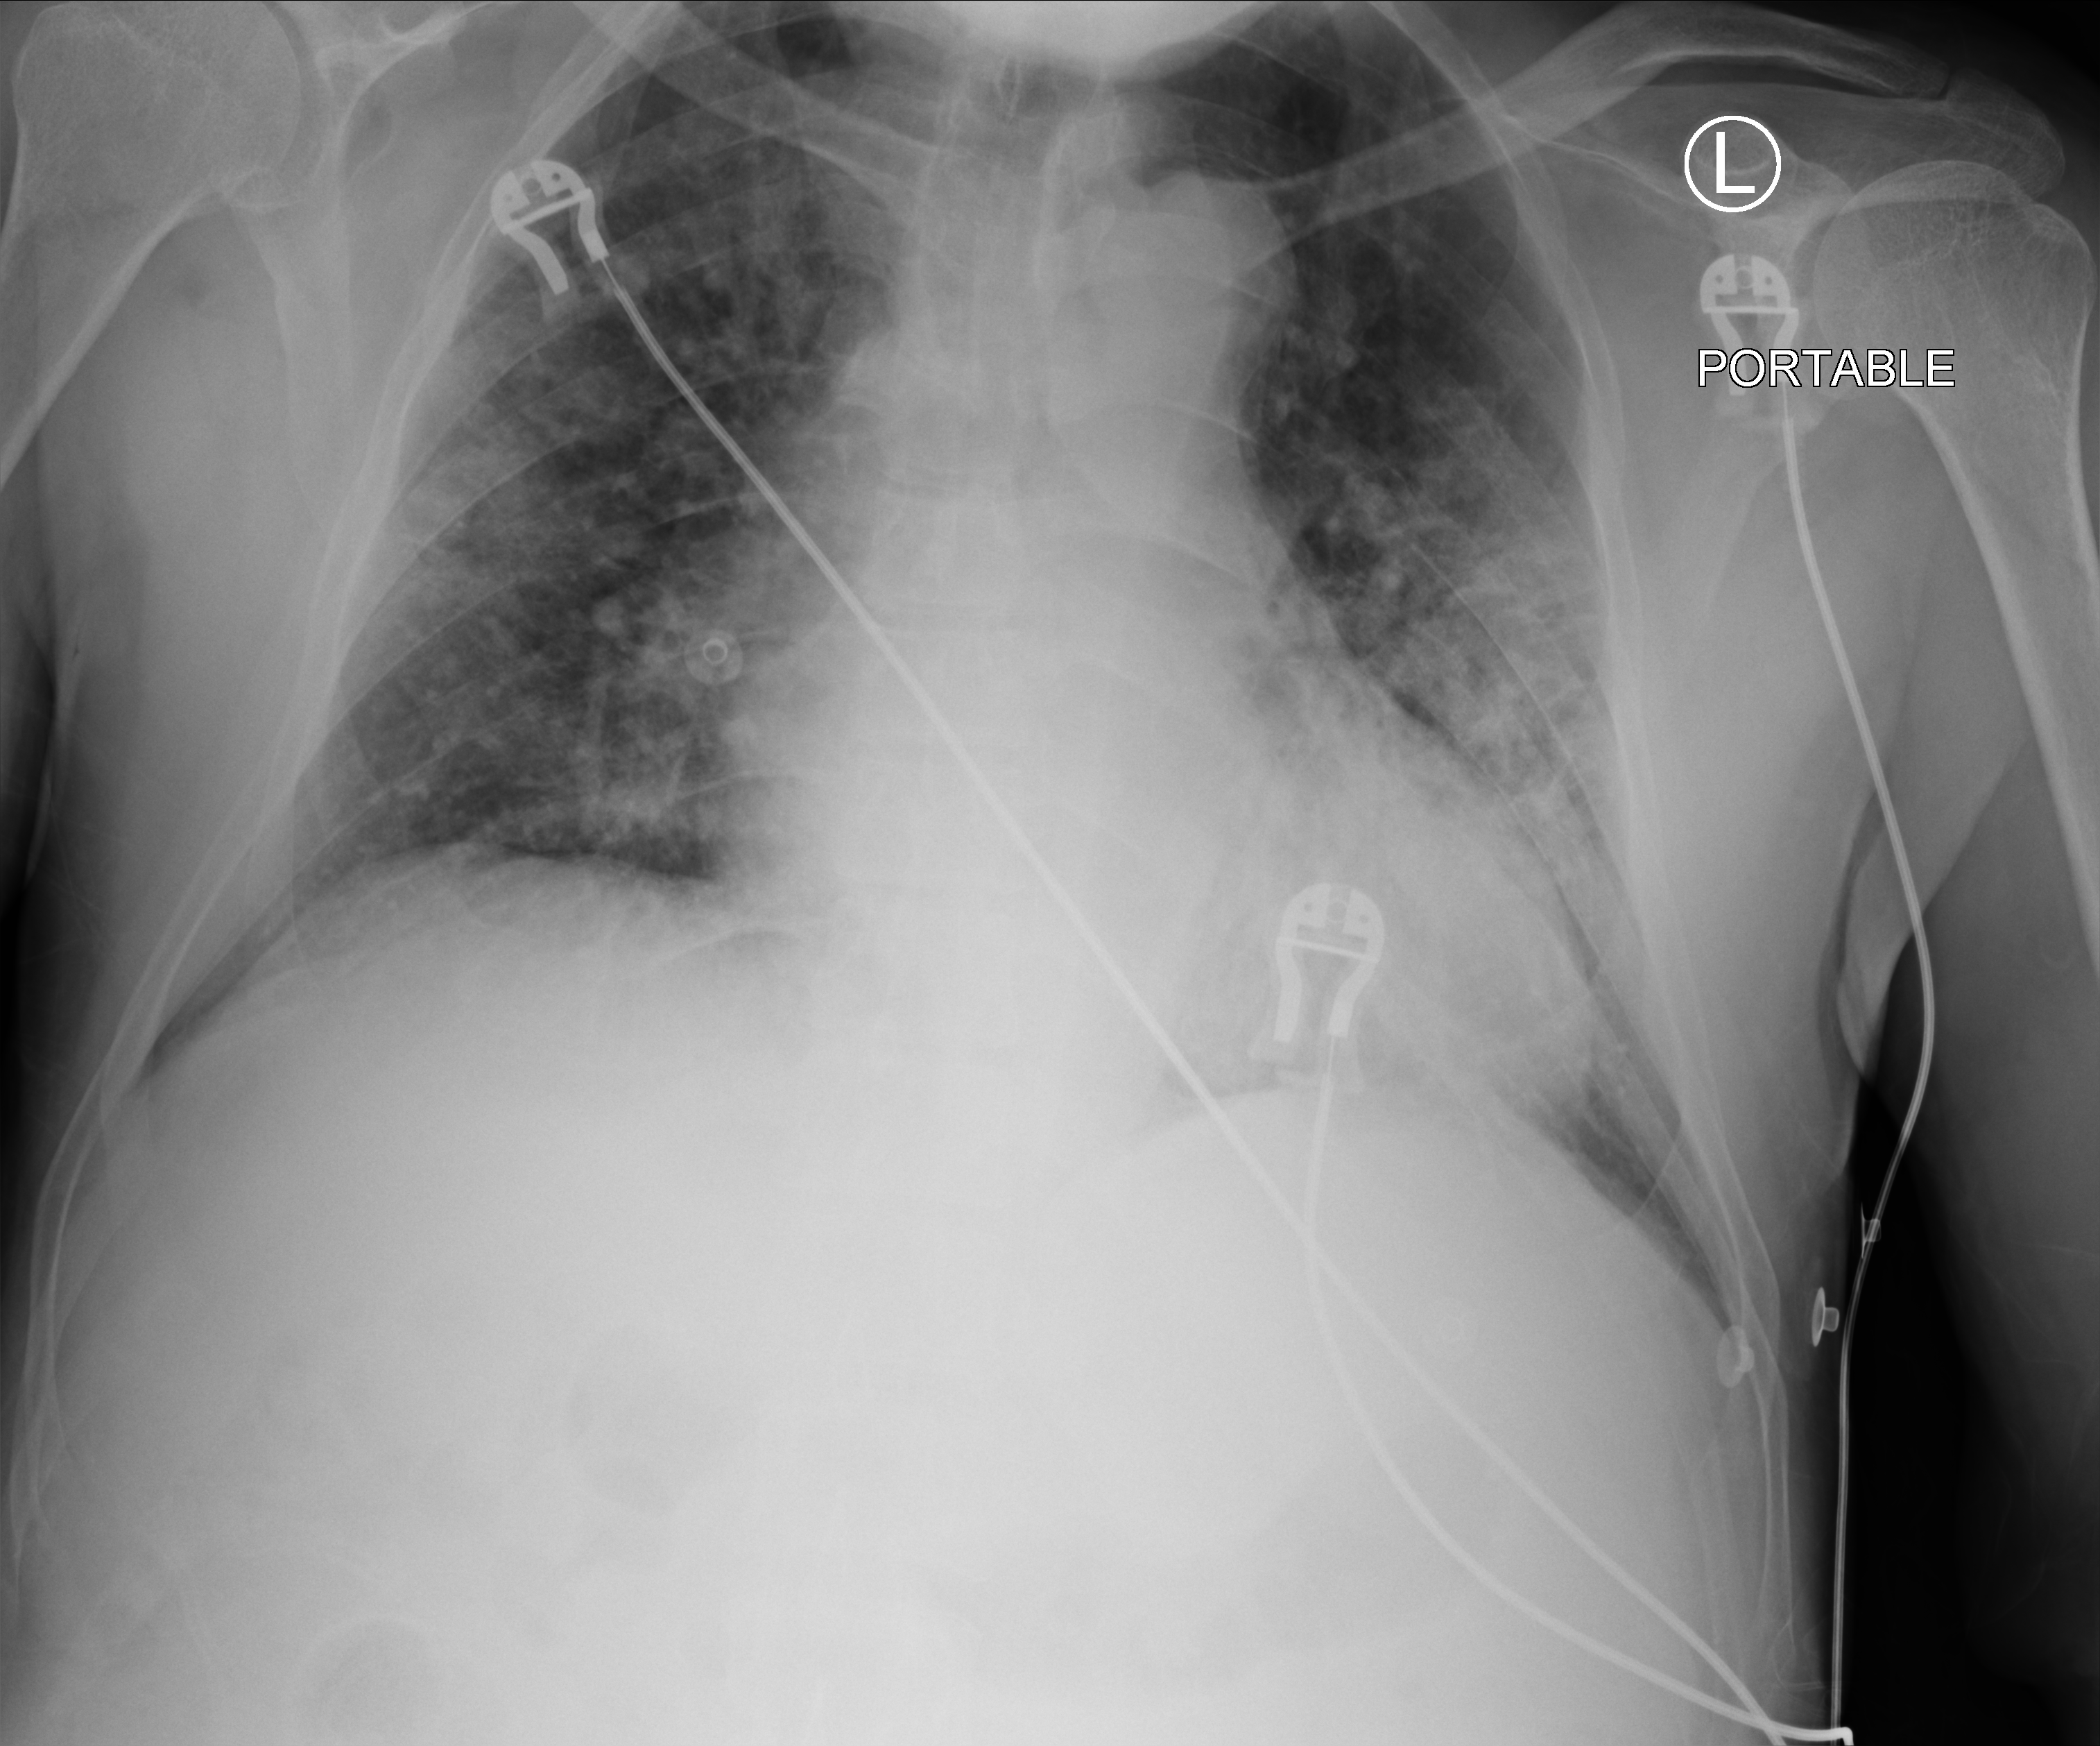
Chest X-ray (portable); anteroposterior (AP) projection. Patient hospitalised with COVID-19; male, aged 60–74 years.
From the hospital-stay record, not from the radiograph (when in the stay this image was taken is not recorded): smoking status (admission record): never; mechanically ventilated during this hospital stay: no.